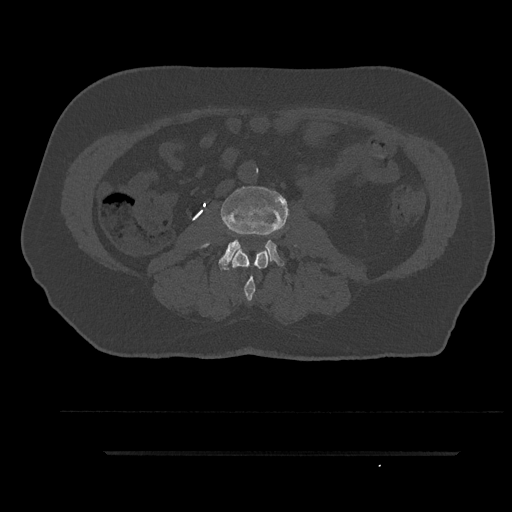
CT including the spine, one axial slice. Position 71 of 797 along the scan axis. Reconstruction kernel Br40s/3. Bone window (W 1800 / L 400 HU). 0.5 mm slice thickness. 512 × 512 image matrix, field of view 432 × 432 mm. Patient: male, 63 years. Case-level facts recorded for this patient, not image findings: primary cancer: renal.
Annotated regions visible in this slice (semi-automatic segmentation, software-assisted and operator-edited):
- L2 vertebra: bounding box <232,250,268,301> (left, top, right, bottom; pixels)
- L3 vertebra: <204,185,289,270>